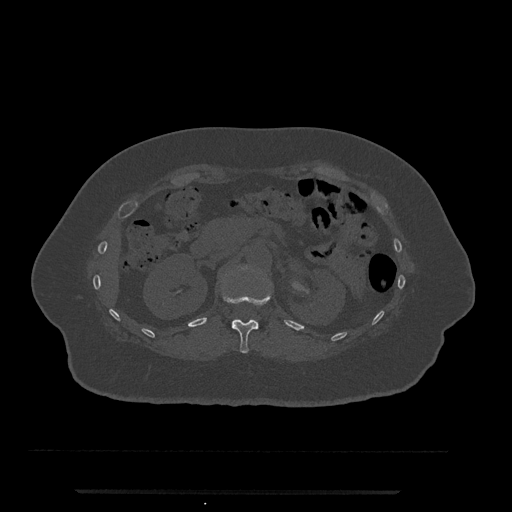
CT including the spine, one axial slice. Slice 148 of 797 in the series (ordered by position). Bone window (W 1800 / L 400 HU). 512 × 512 image matrix, field of view 440 × 440 mm. Female patient, age 51 years. Case-level facts recorded for this patient, not image findings: primary cancer: neuro; vertebrae with lytic lesions (as recorded): T8.
Structures marked on this image (semi-automatically segmented with operator editing):
- L1 vertebra: bounding box [x1, y1, x2, y2] px = [244, 265, 250, 269]
- T12 vertebra: [222, 291, 271, 353]